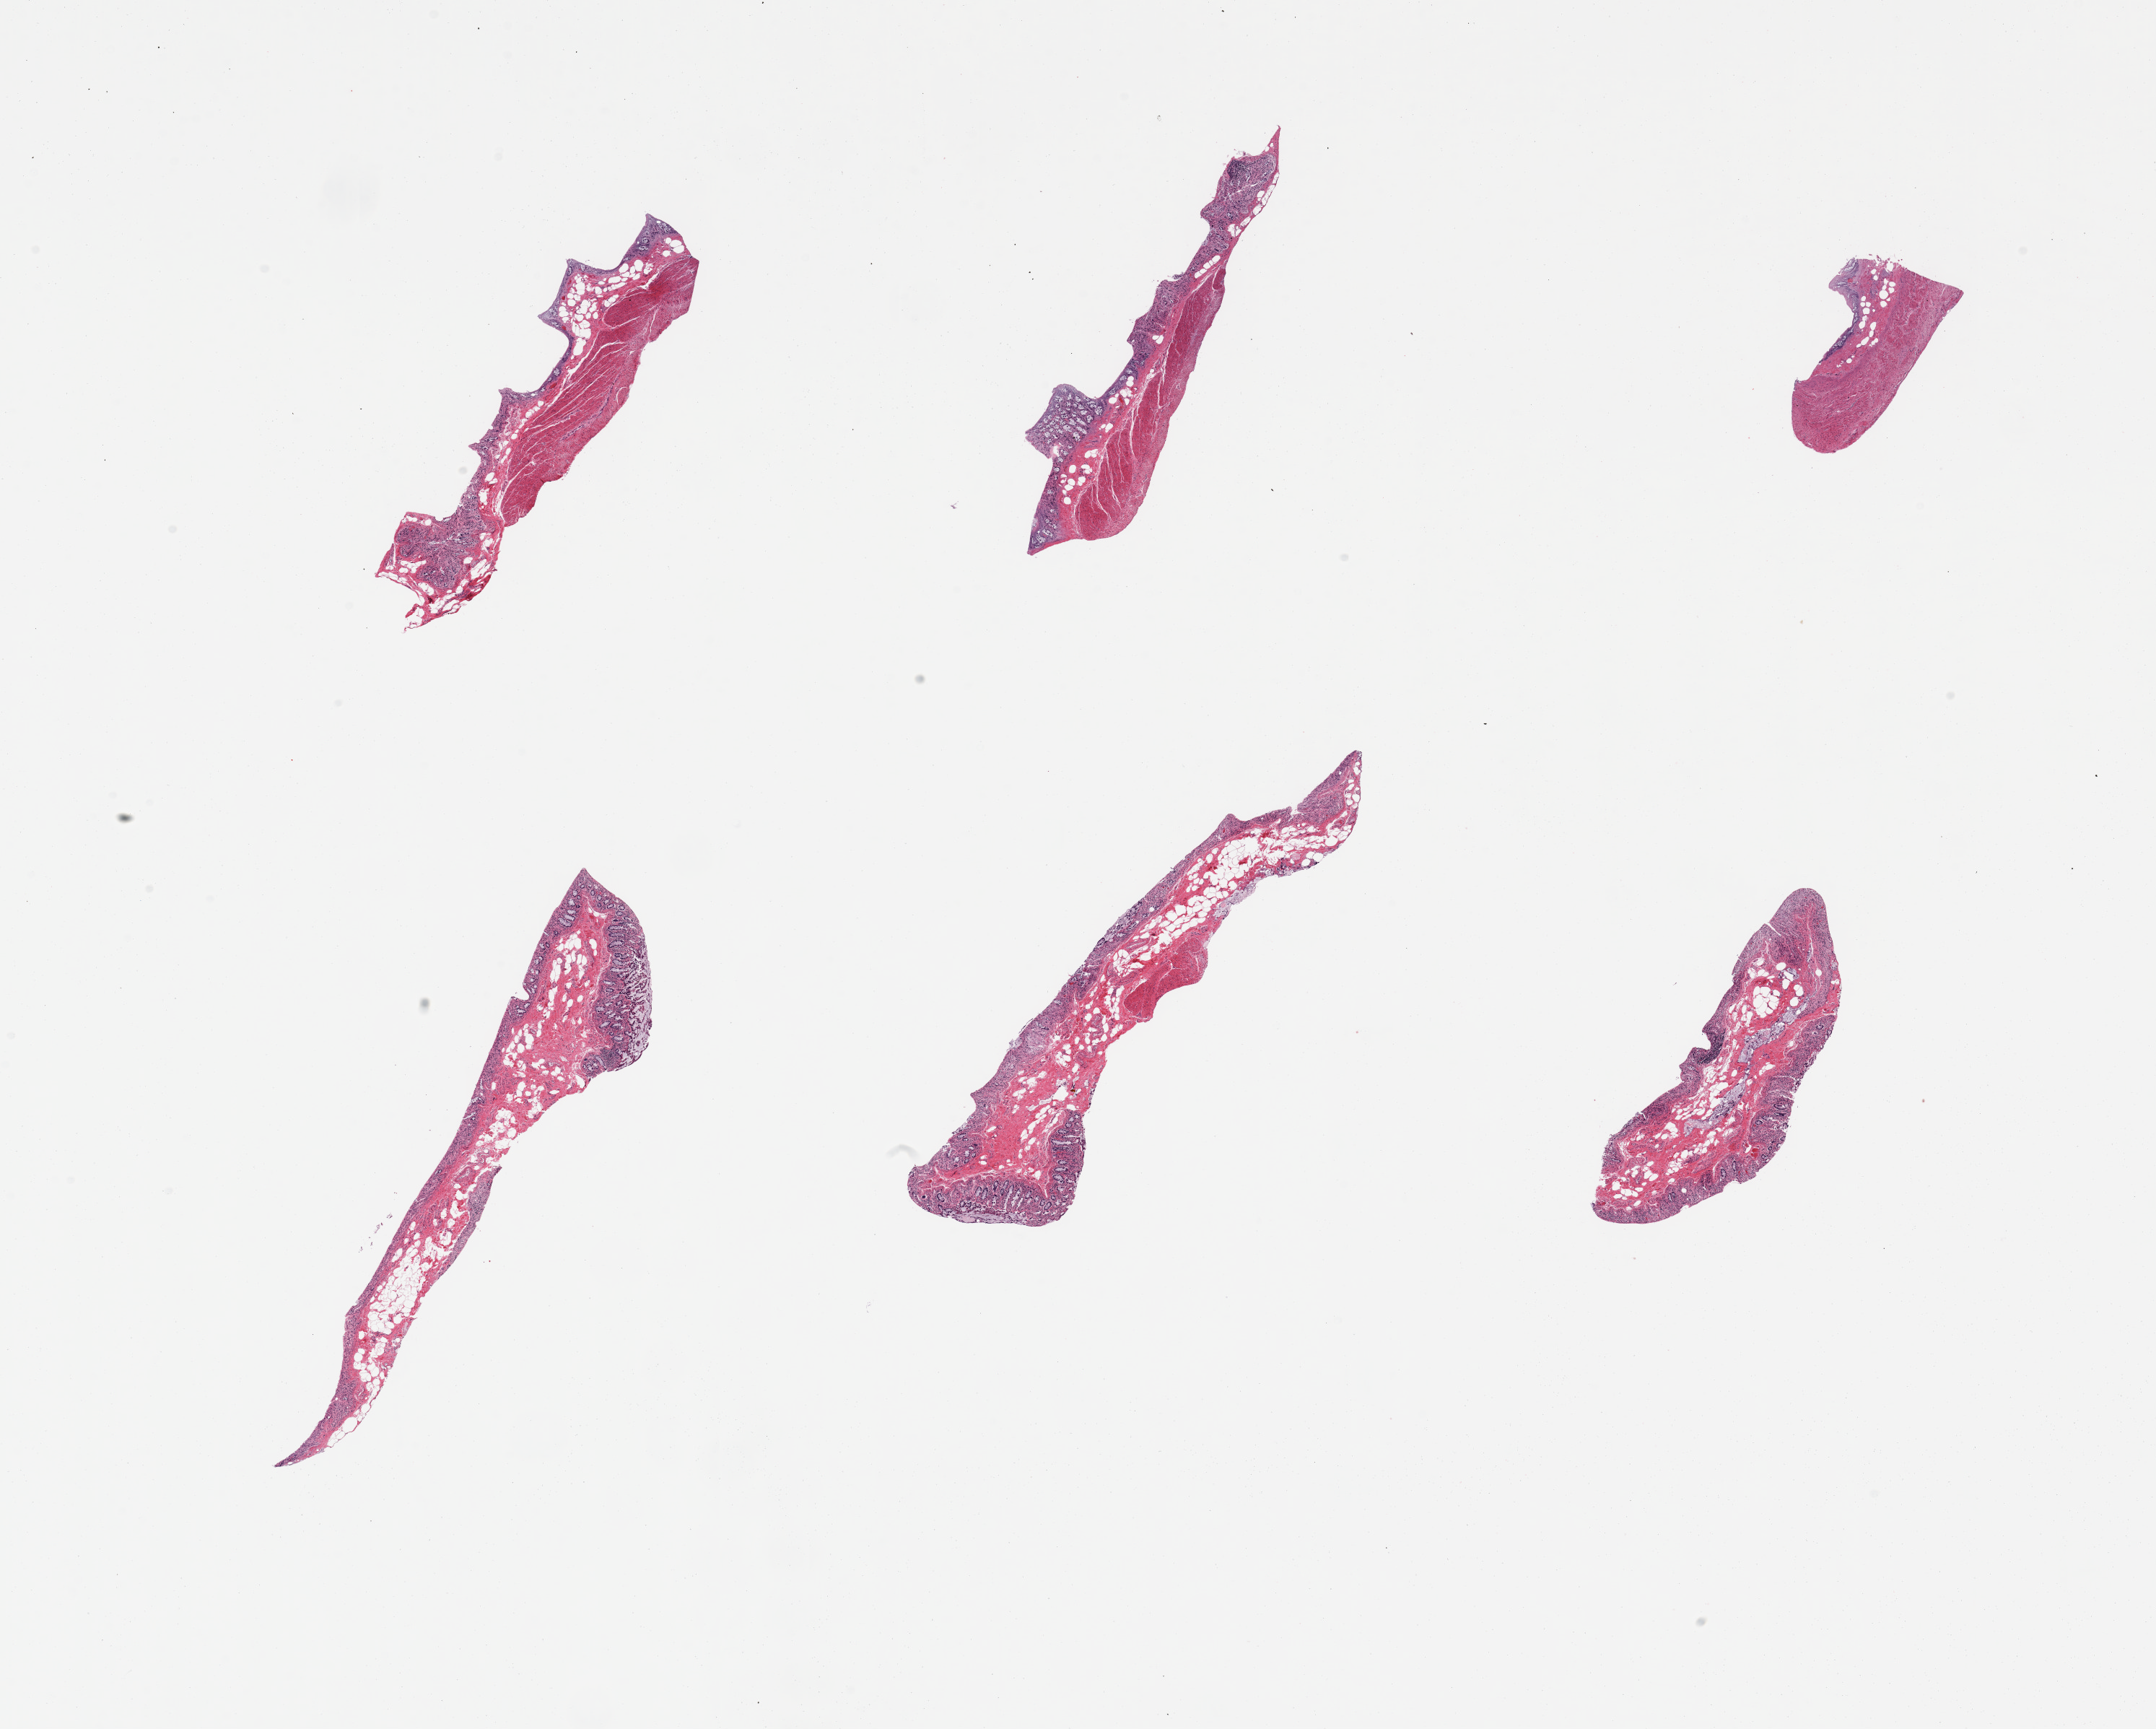
H&E whole-slide image — a low-resolution overview of the entire scanned area, about 23.6 x 18.9 mm (acquisition: 20x scan). PAXgene-fixed, paraffin-embedded tissue. Sampled site (target tissue): transverse colon. Donor tissue sample.
• pathologist's review note for this sample: 6 pieces; autolyzed mucosa and preserved muscularis on 3 of 6 samples